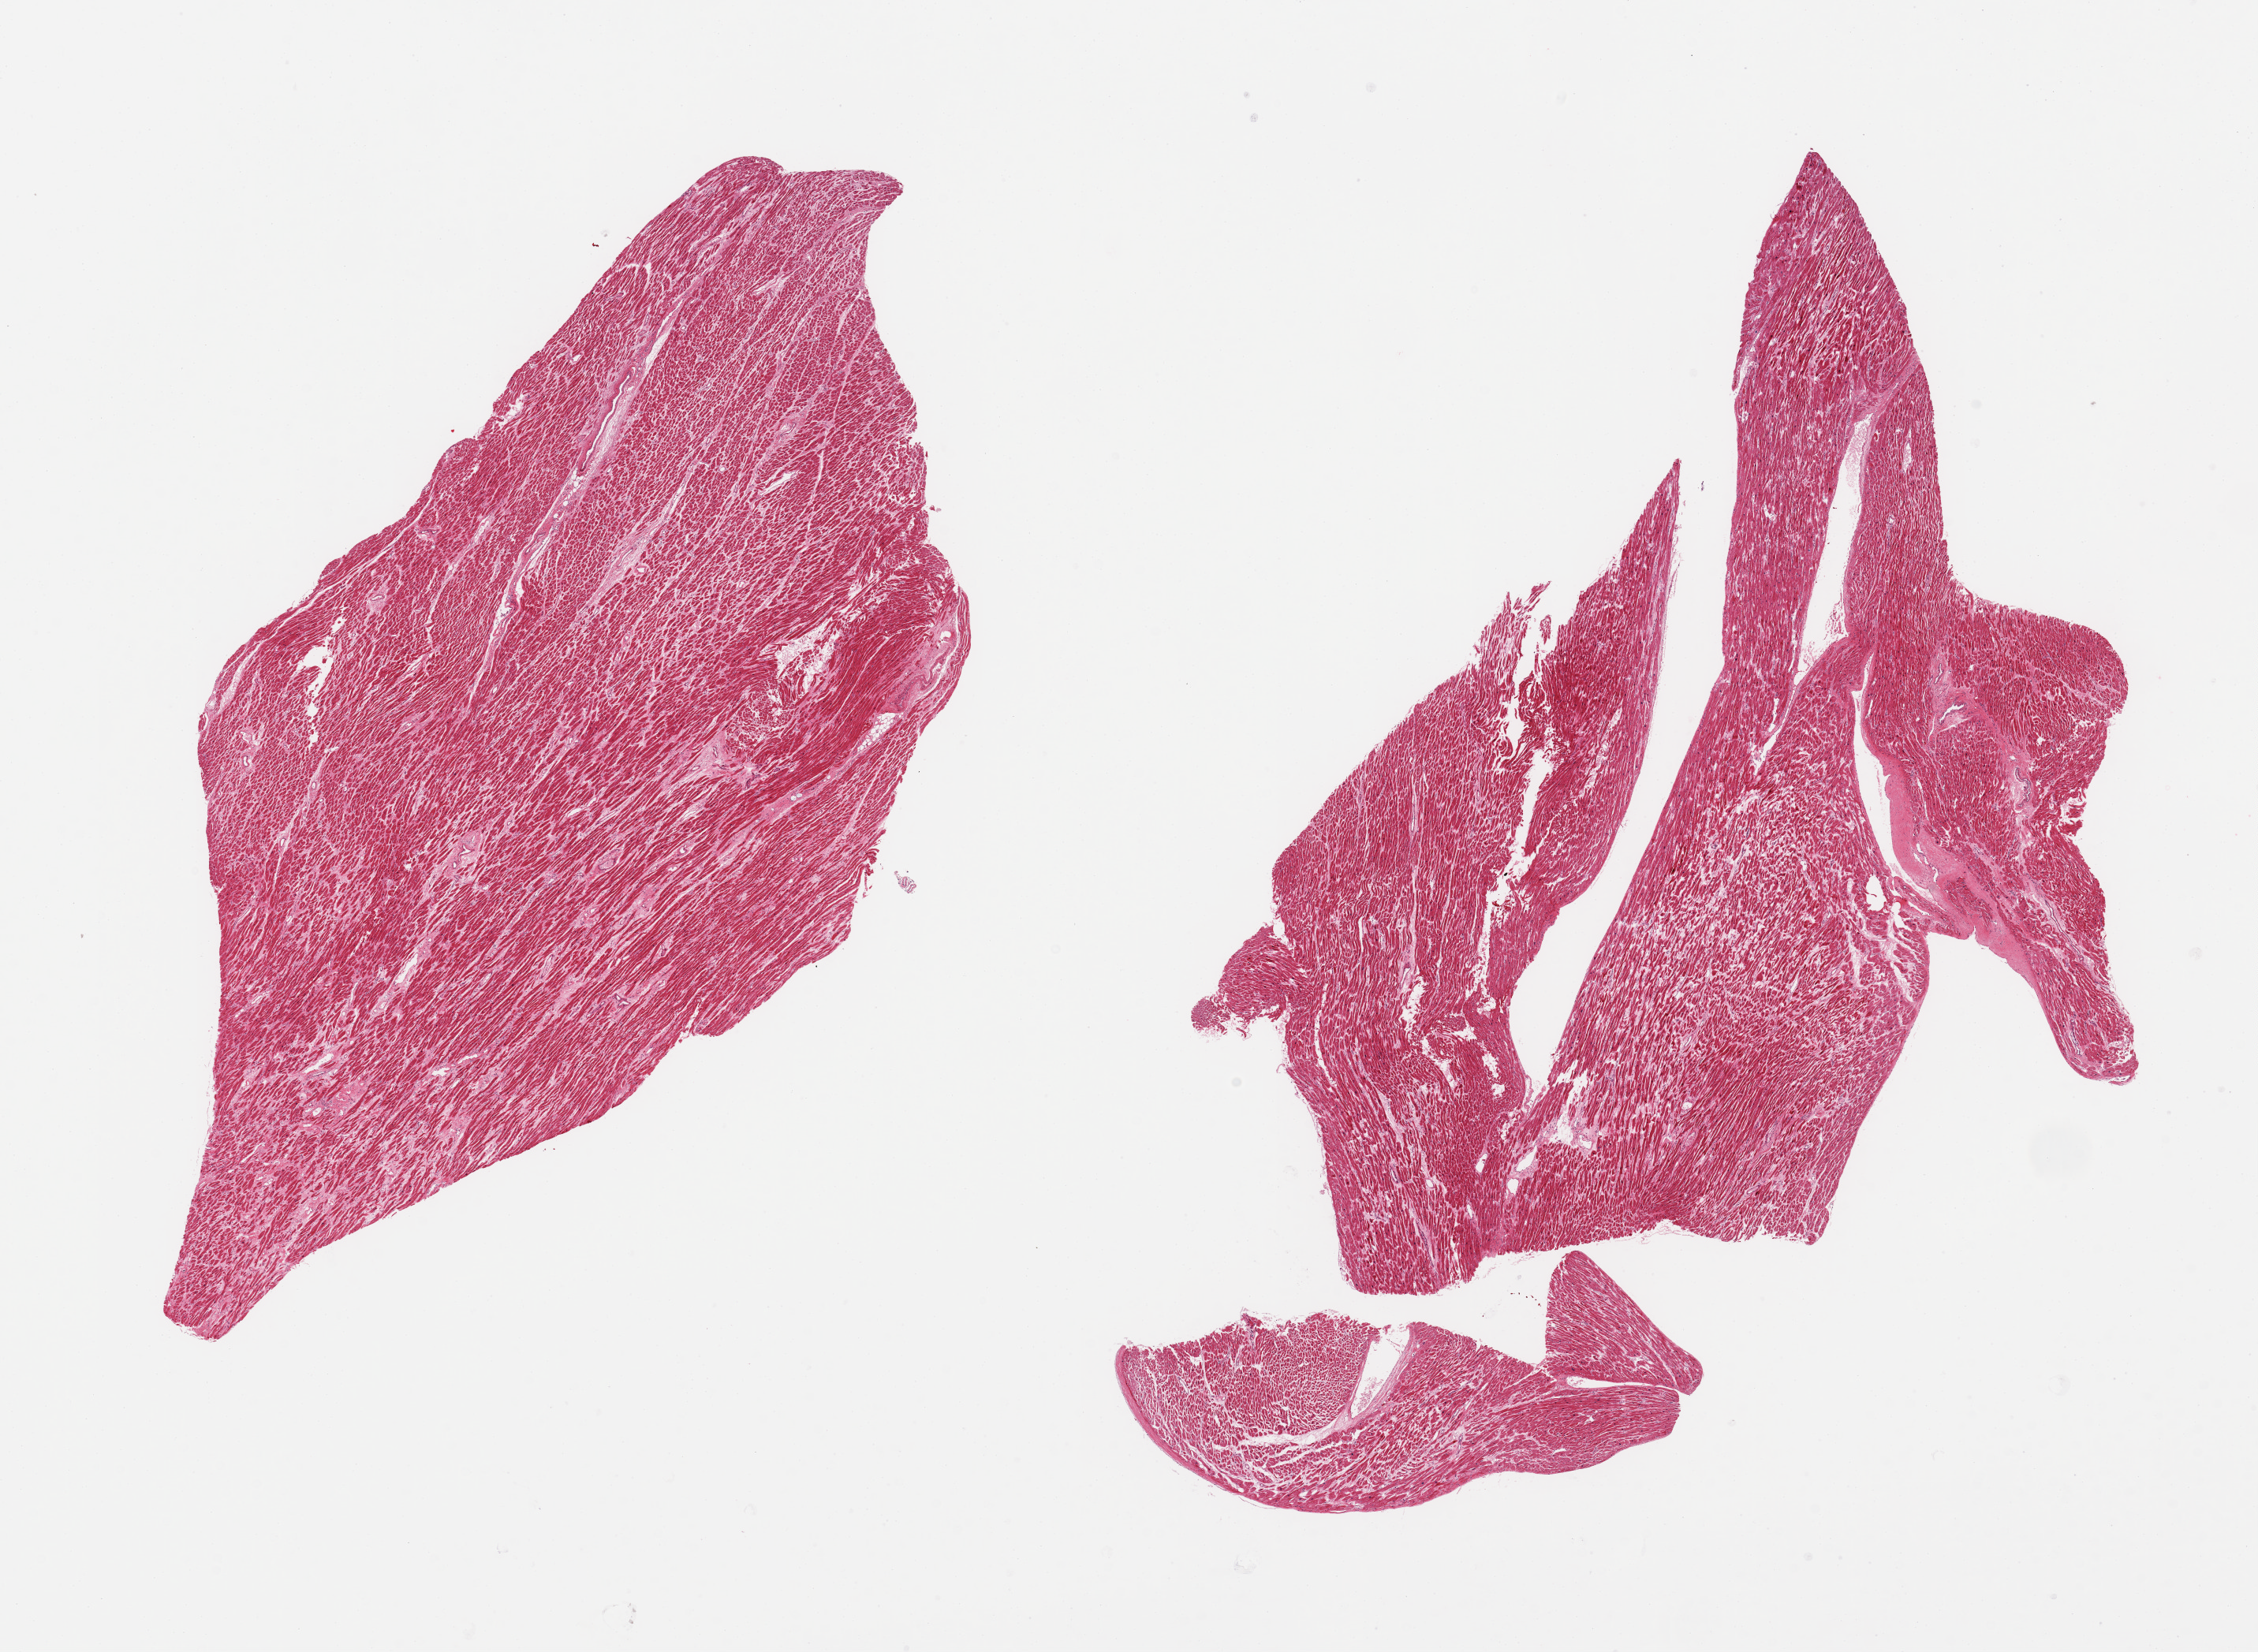
Whole-slide image, haematoxylin and eosin stain — whole scanned area (about 22.6 x 16.6 mm) shown as a low-resolution overview; PAXgene-fixed paraffin-embedded (PFPE) section; sampled site (target tissue): auricular appendage; tissue donor sample. Male donor.
Reviewer comment on this tissue sample: 2 pieces, no abnormalities.